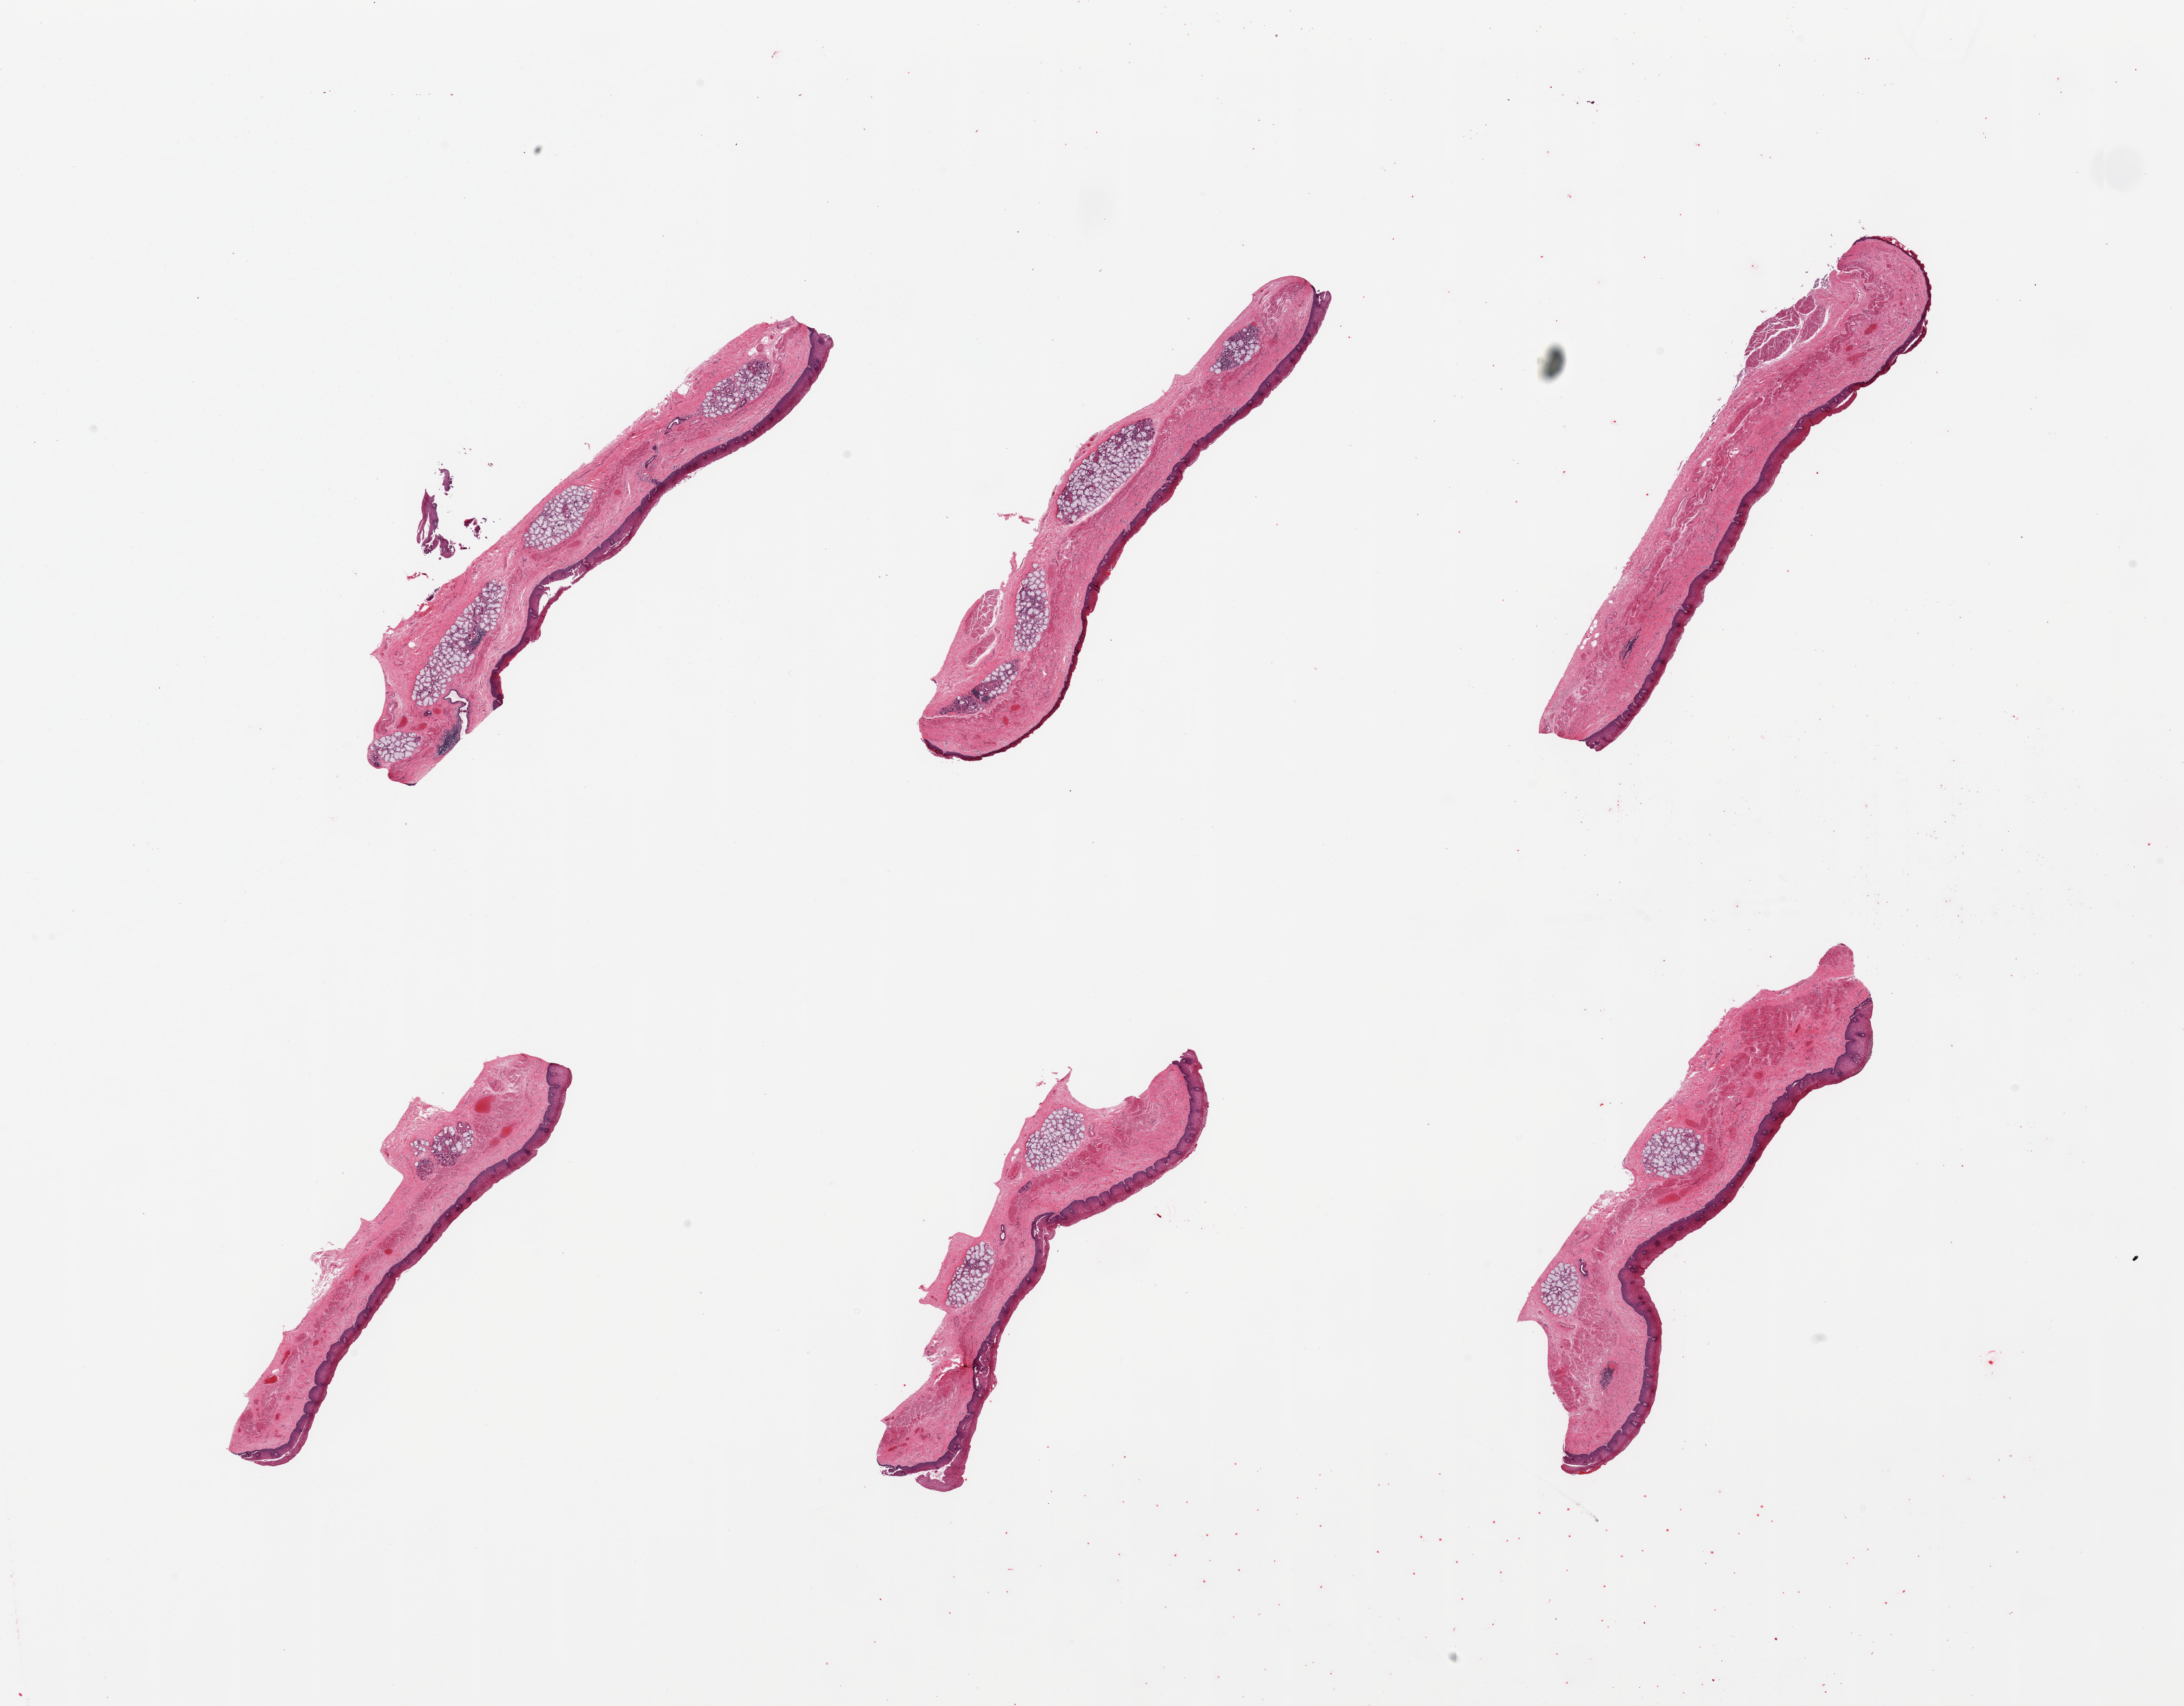
Hematoxylin and eosin (H&E) whole-slide image — low-resolution overview of the scanned area, about 26.6 x 20.8 mm (slide scanned at 20x); PAXgene-fixed paraffin-embedded (PFPE) section; section of esophageal mucous membrane (target tissue); tissue donor sample. Donor sex: male.
Pathologist's review note for this sample: 6 pieces; includes submucosal glands in 5 pieces; squamous mucosa up to 0.15mm.